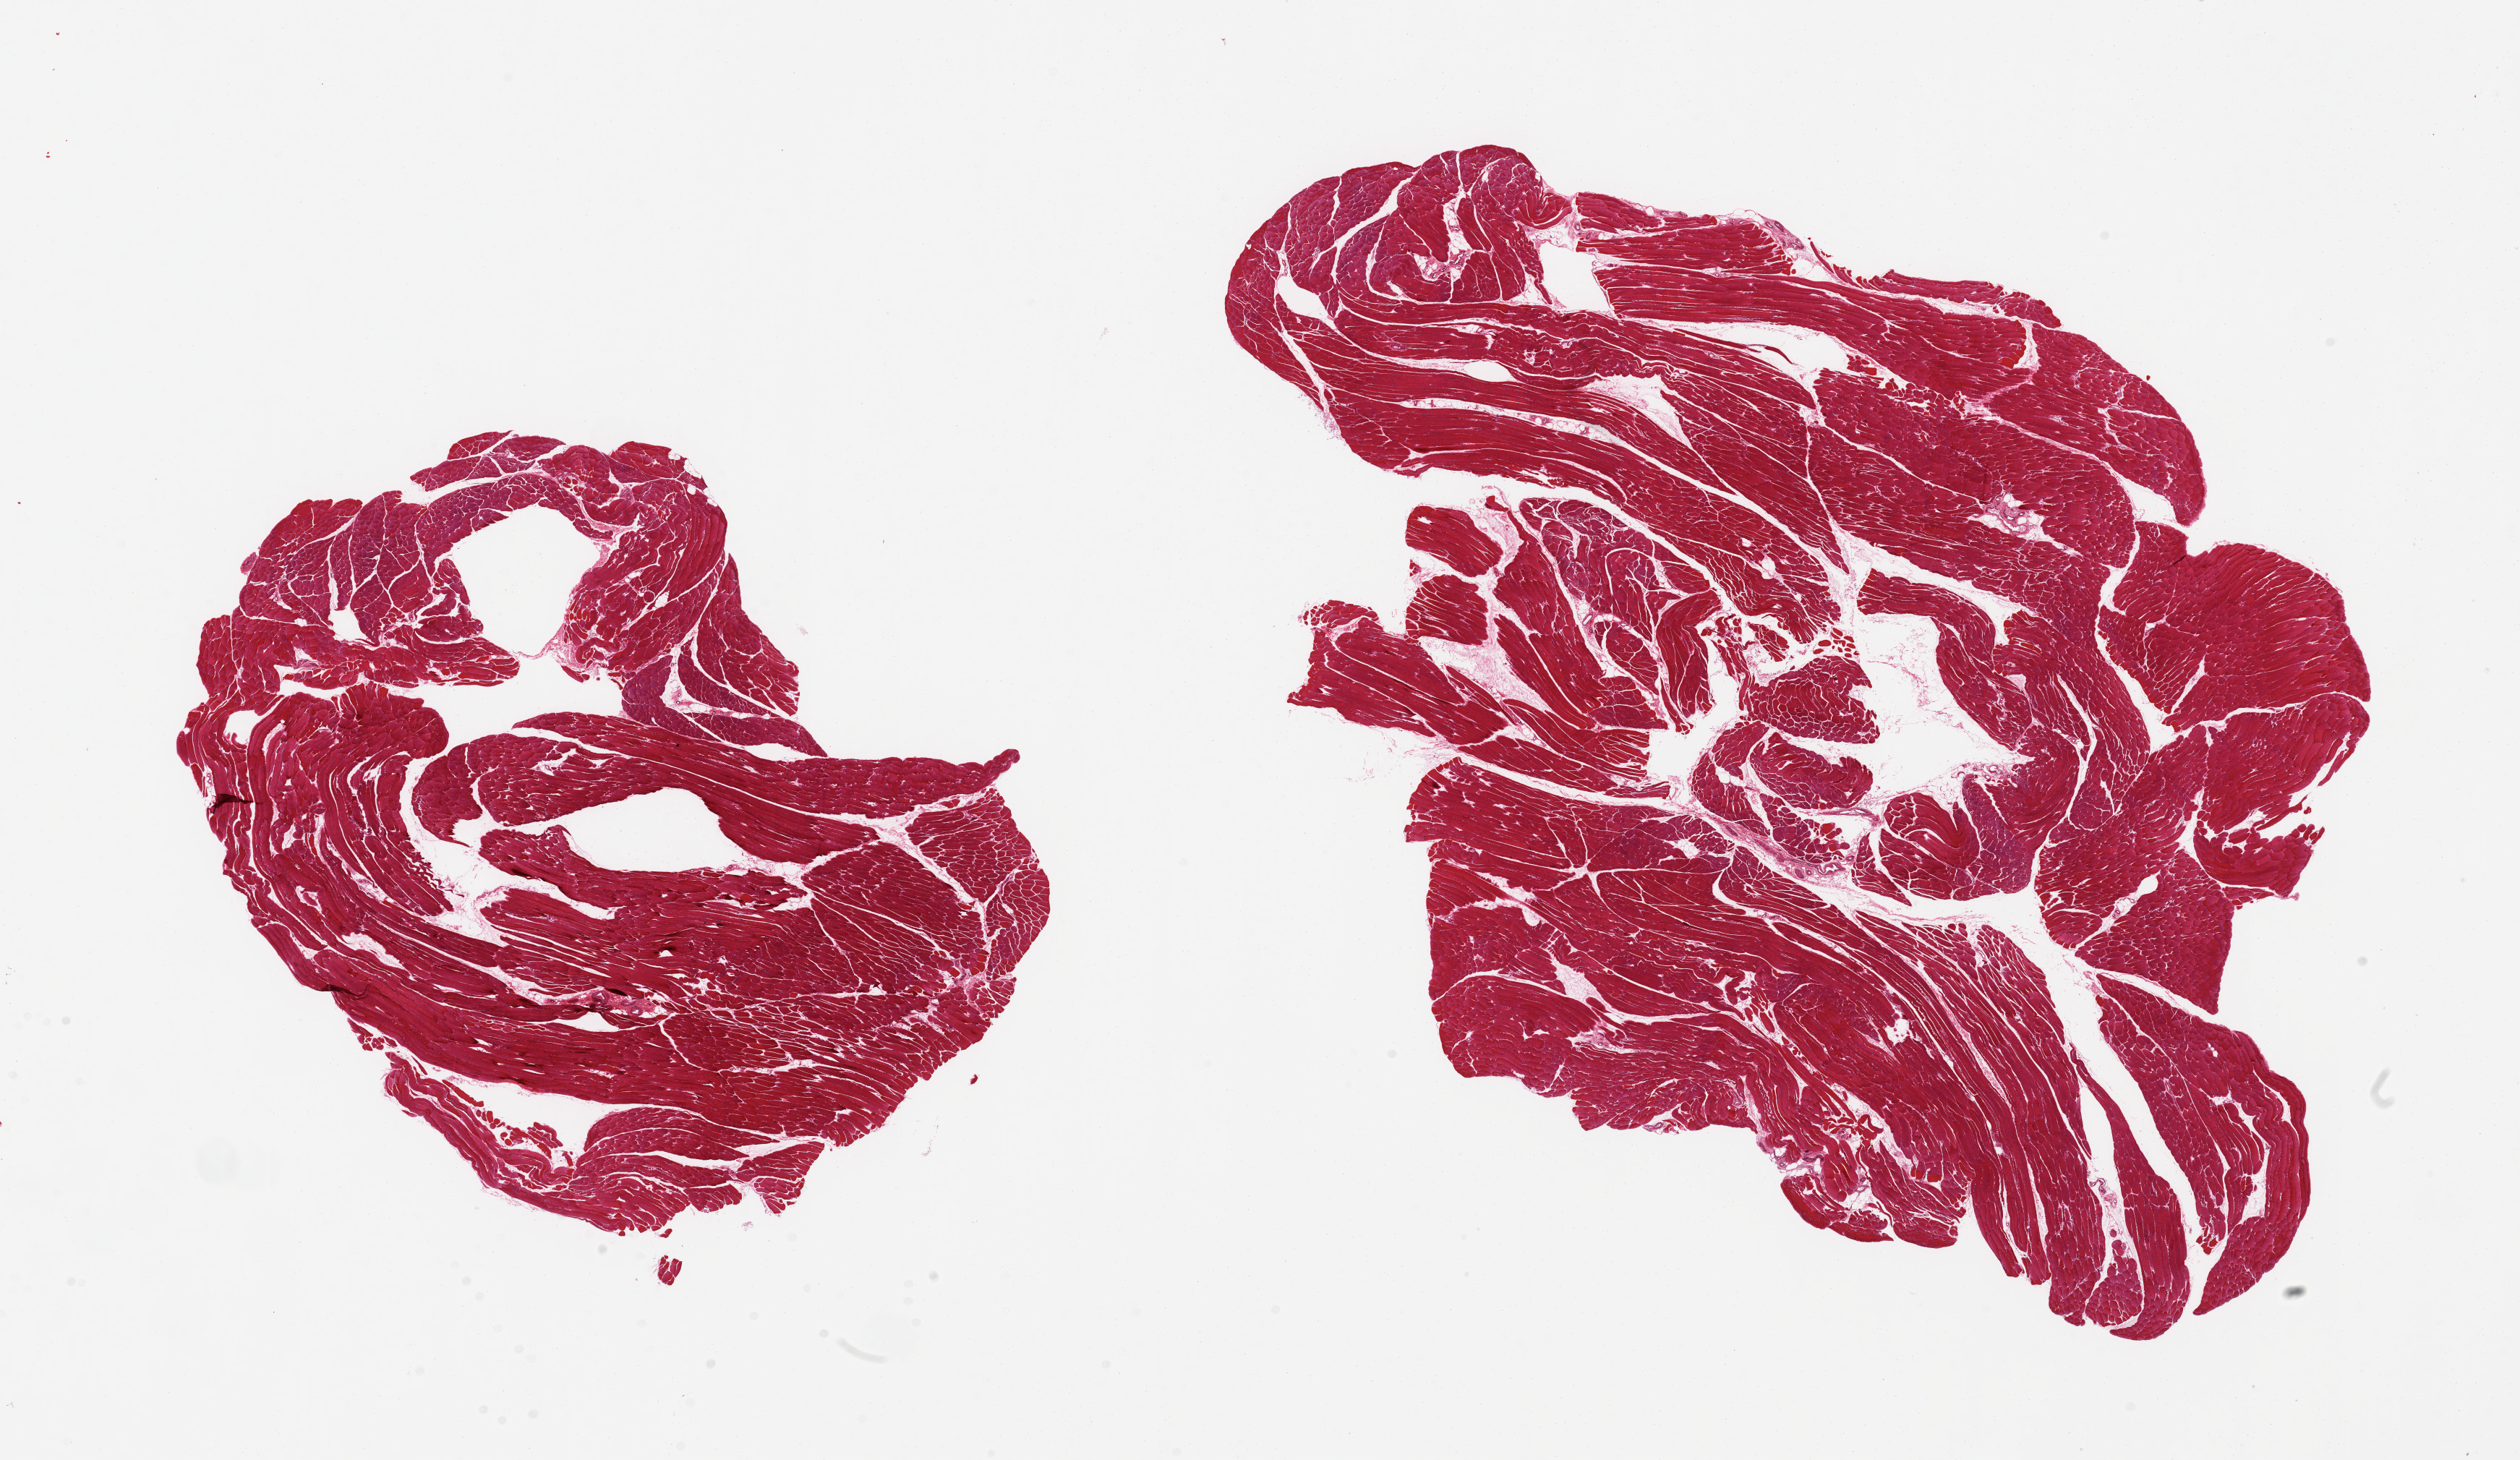
Hematoxylin and eosin (H&E) whole-slide image, low-resolution overview of the scanned area, about 27.6 x 16.0 mm; PAXgene-fixed, paraffin-embedded tissue; sampled site (target tissue): skeletal muscle; tissue donor sample. Female donor.
Pathologist's review note for this sample: 2 pieces.